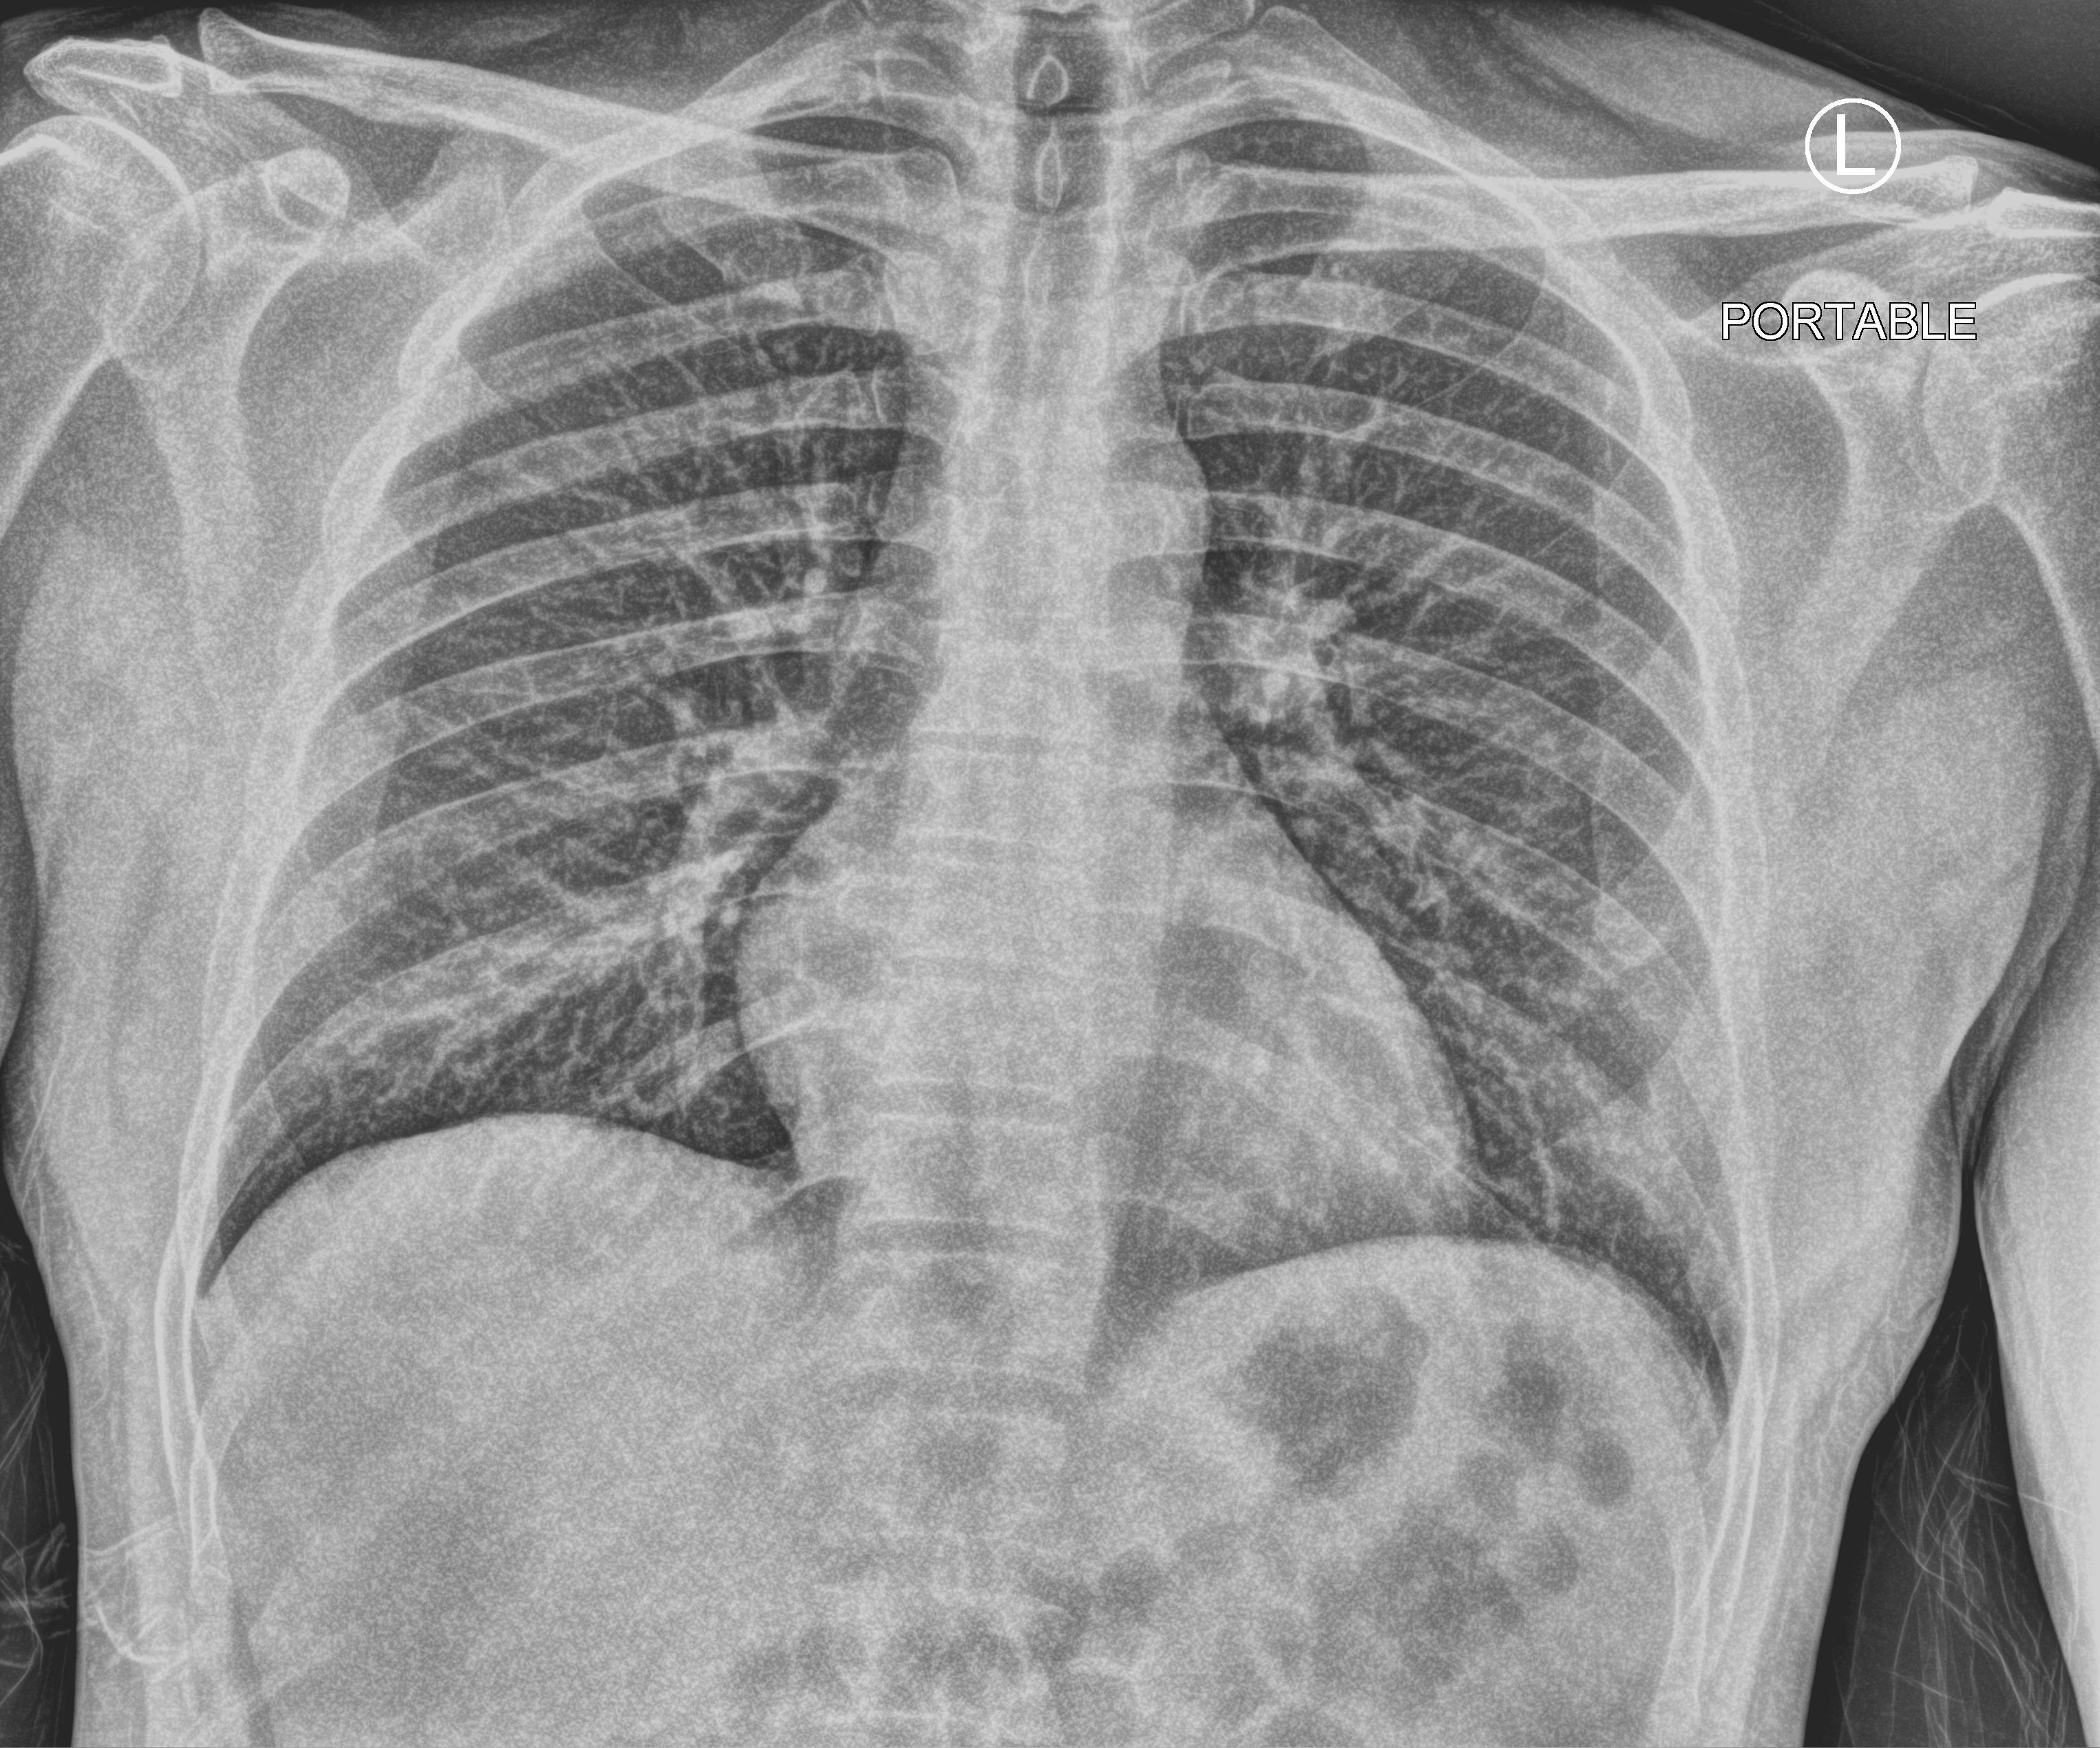
Portable chest radiograph. Patient hospitalised with COVID-19; male, aged 18–59 years.
Admission-level facts for this patient (not findings on this image; timing relative to this image not recorded): other chronic lung disease (admission record): no.